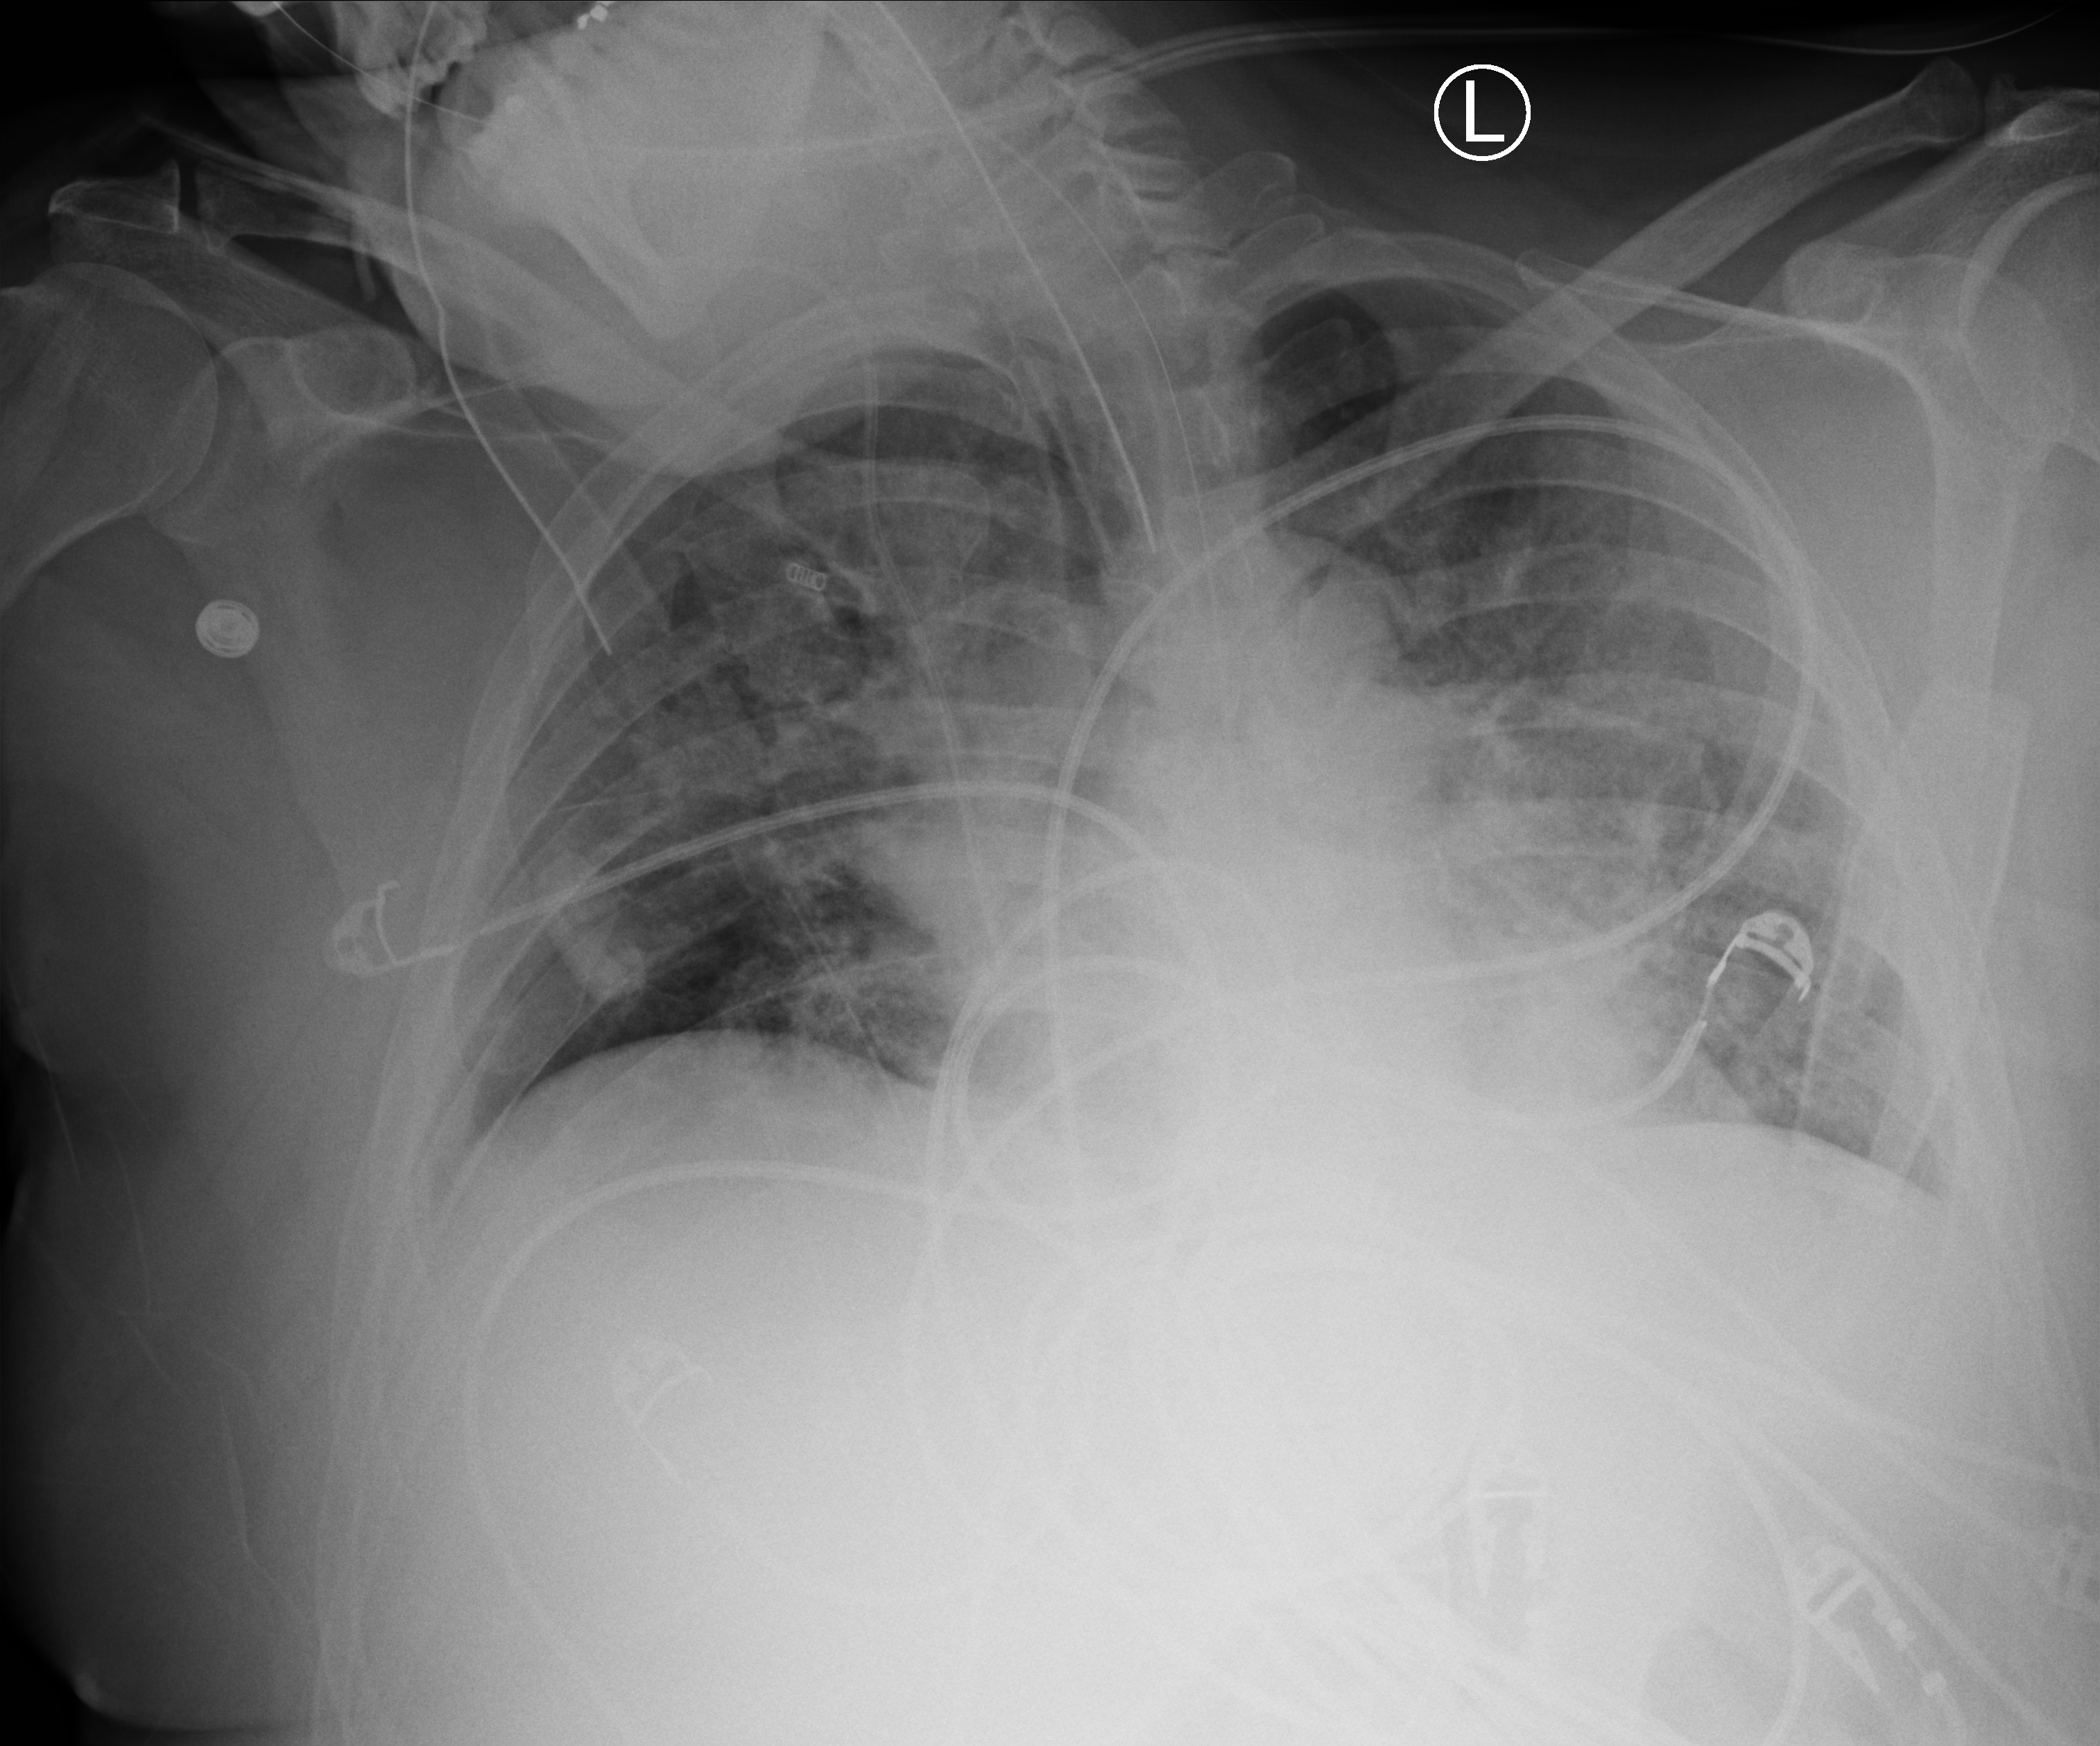
Chest X-ray (portable); anteroposterior (AP) projection. Patient hospitalised with COVID-19; male, aged 18–59 years.
Admission-level facts for this patient (not findings on this image; timing relative to this image not recorded): smoking status (admission record): former; admitted to intensive care during this hospital stay: yes; chronic kidney disease (admission record): no.